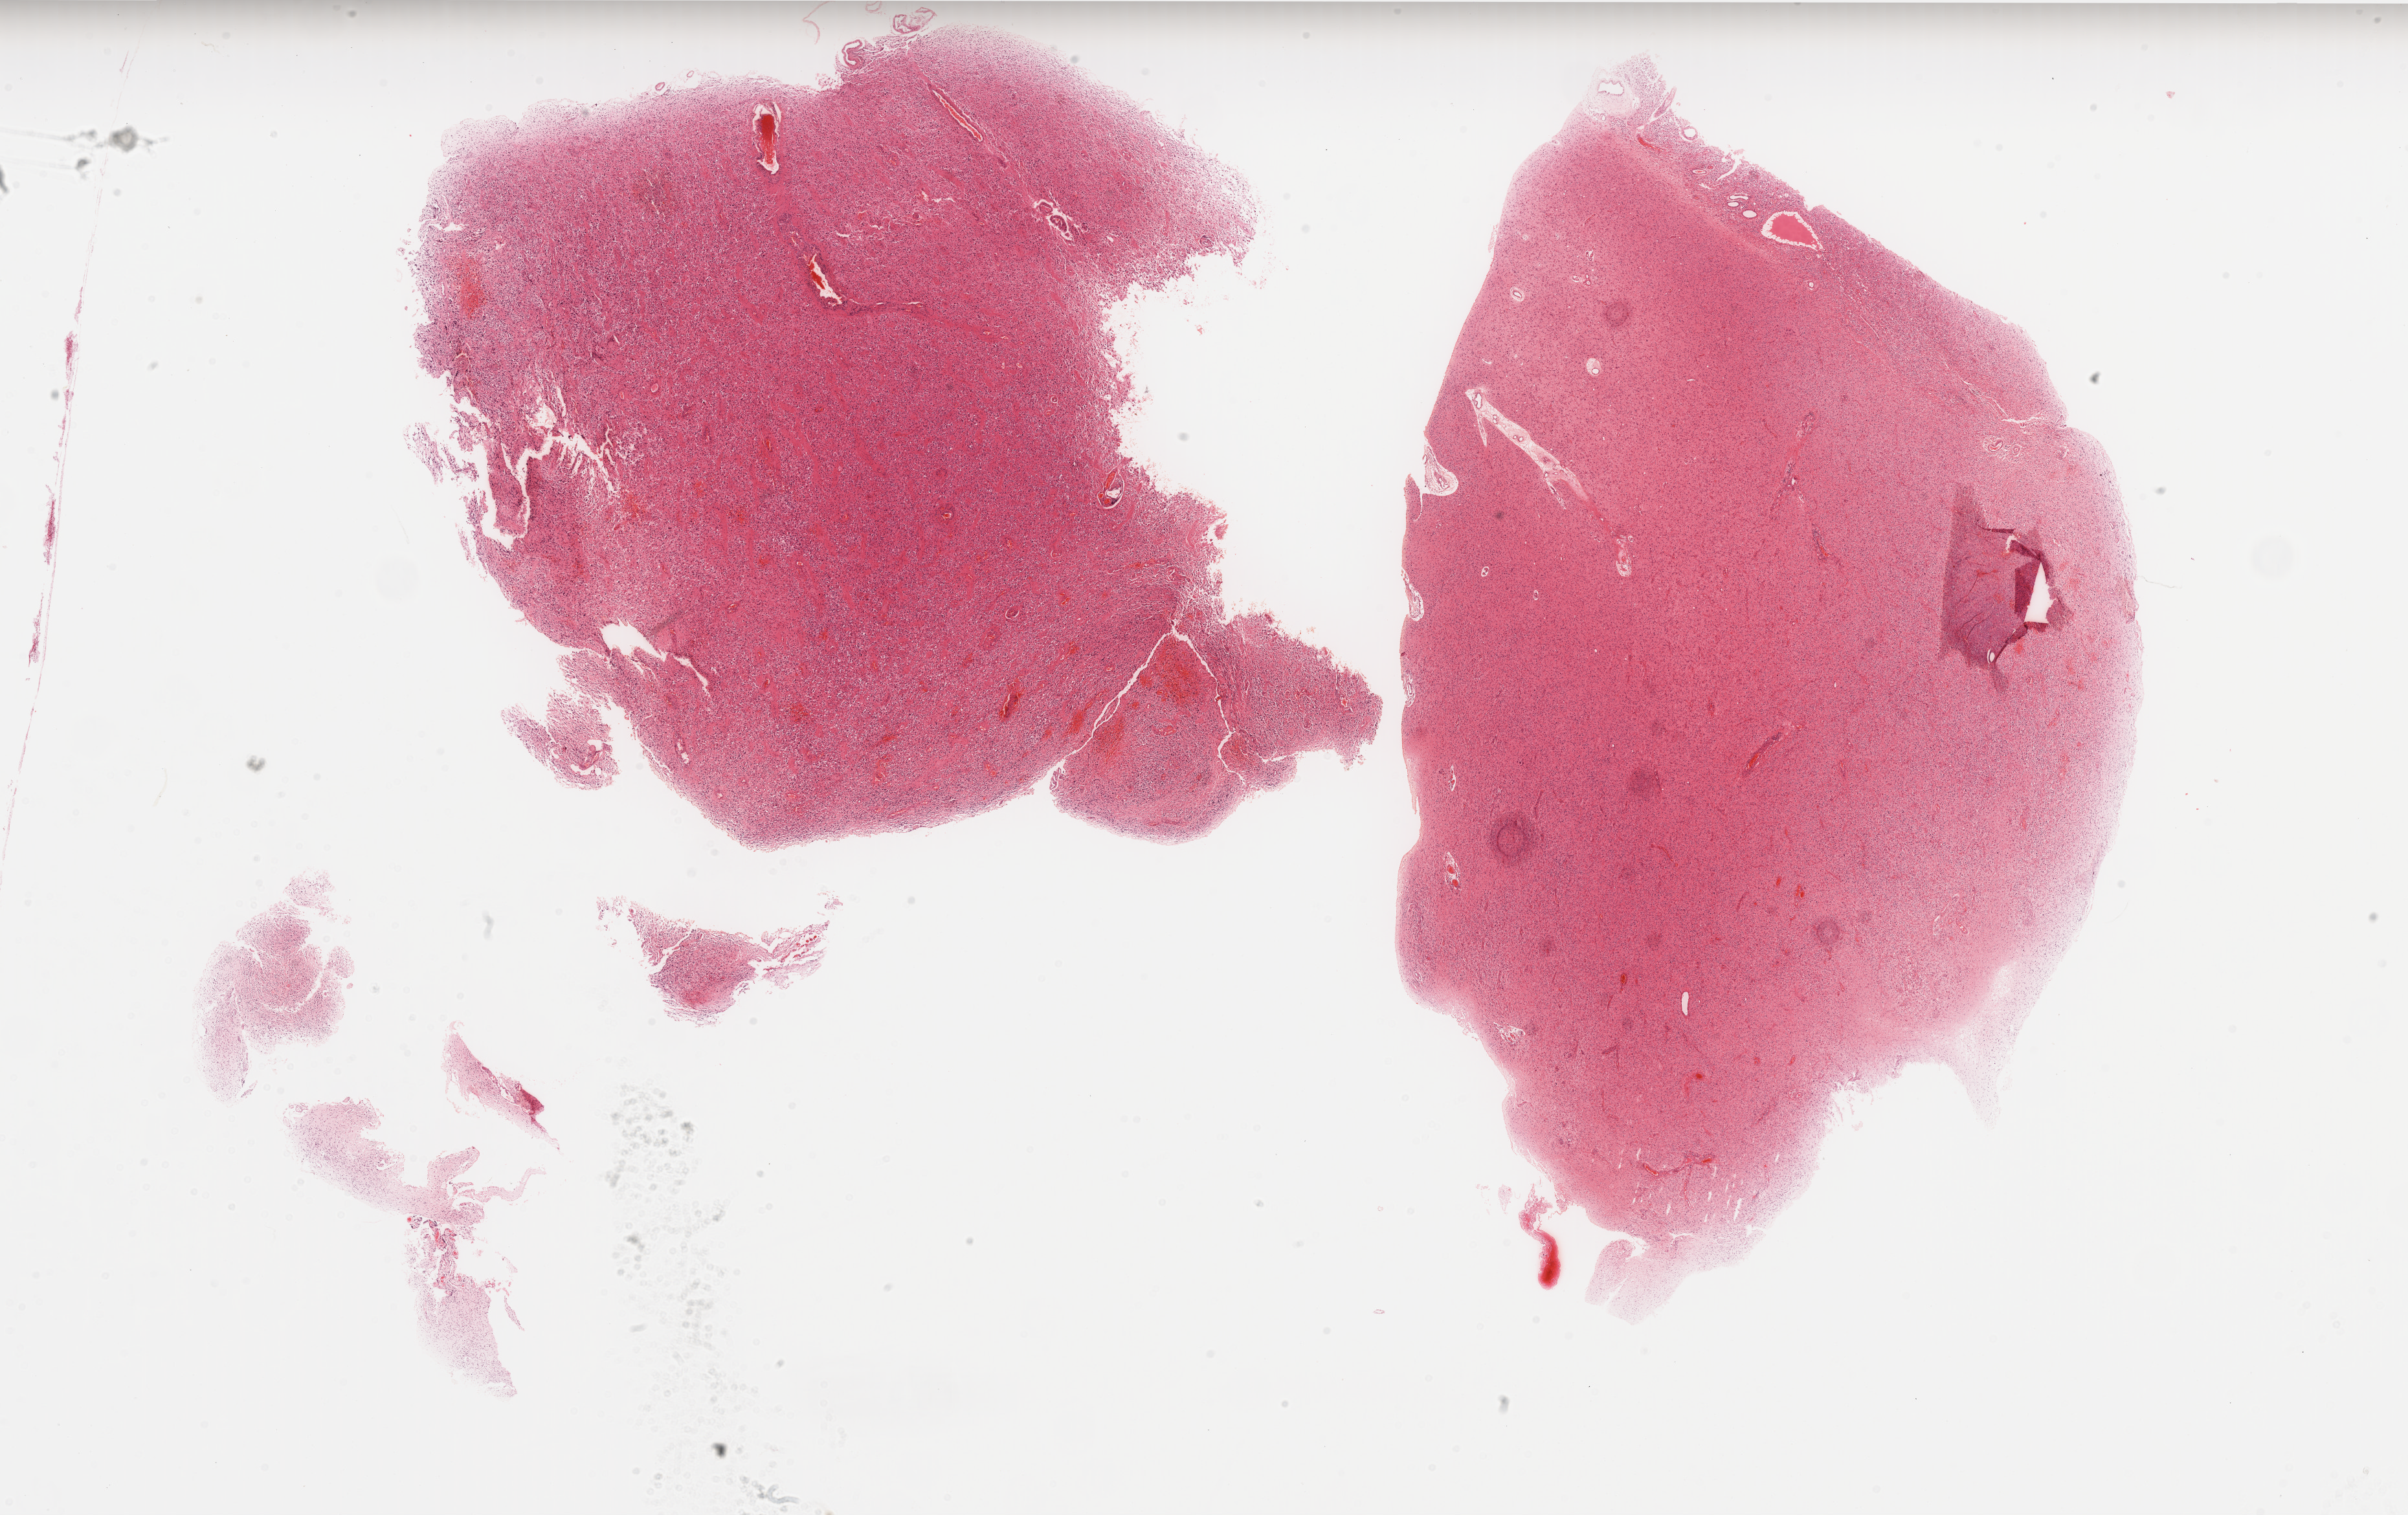
H&E whole-slide image, low-resolution overview of the scanned area, about 29.8 x 18.8 mm, formalin-fixed paraffin-embedded (FFPE) diagnostic section, sample: primary tumour, brain. Female, age 33 years at initial diagnosis. Histologic grade: G3 (poorly differentiated).
Laterality: right. Histologic diagnosis: Astrocytoma, anaplastic (cerebrum).